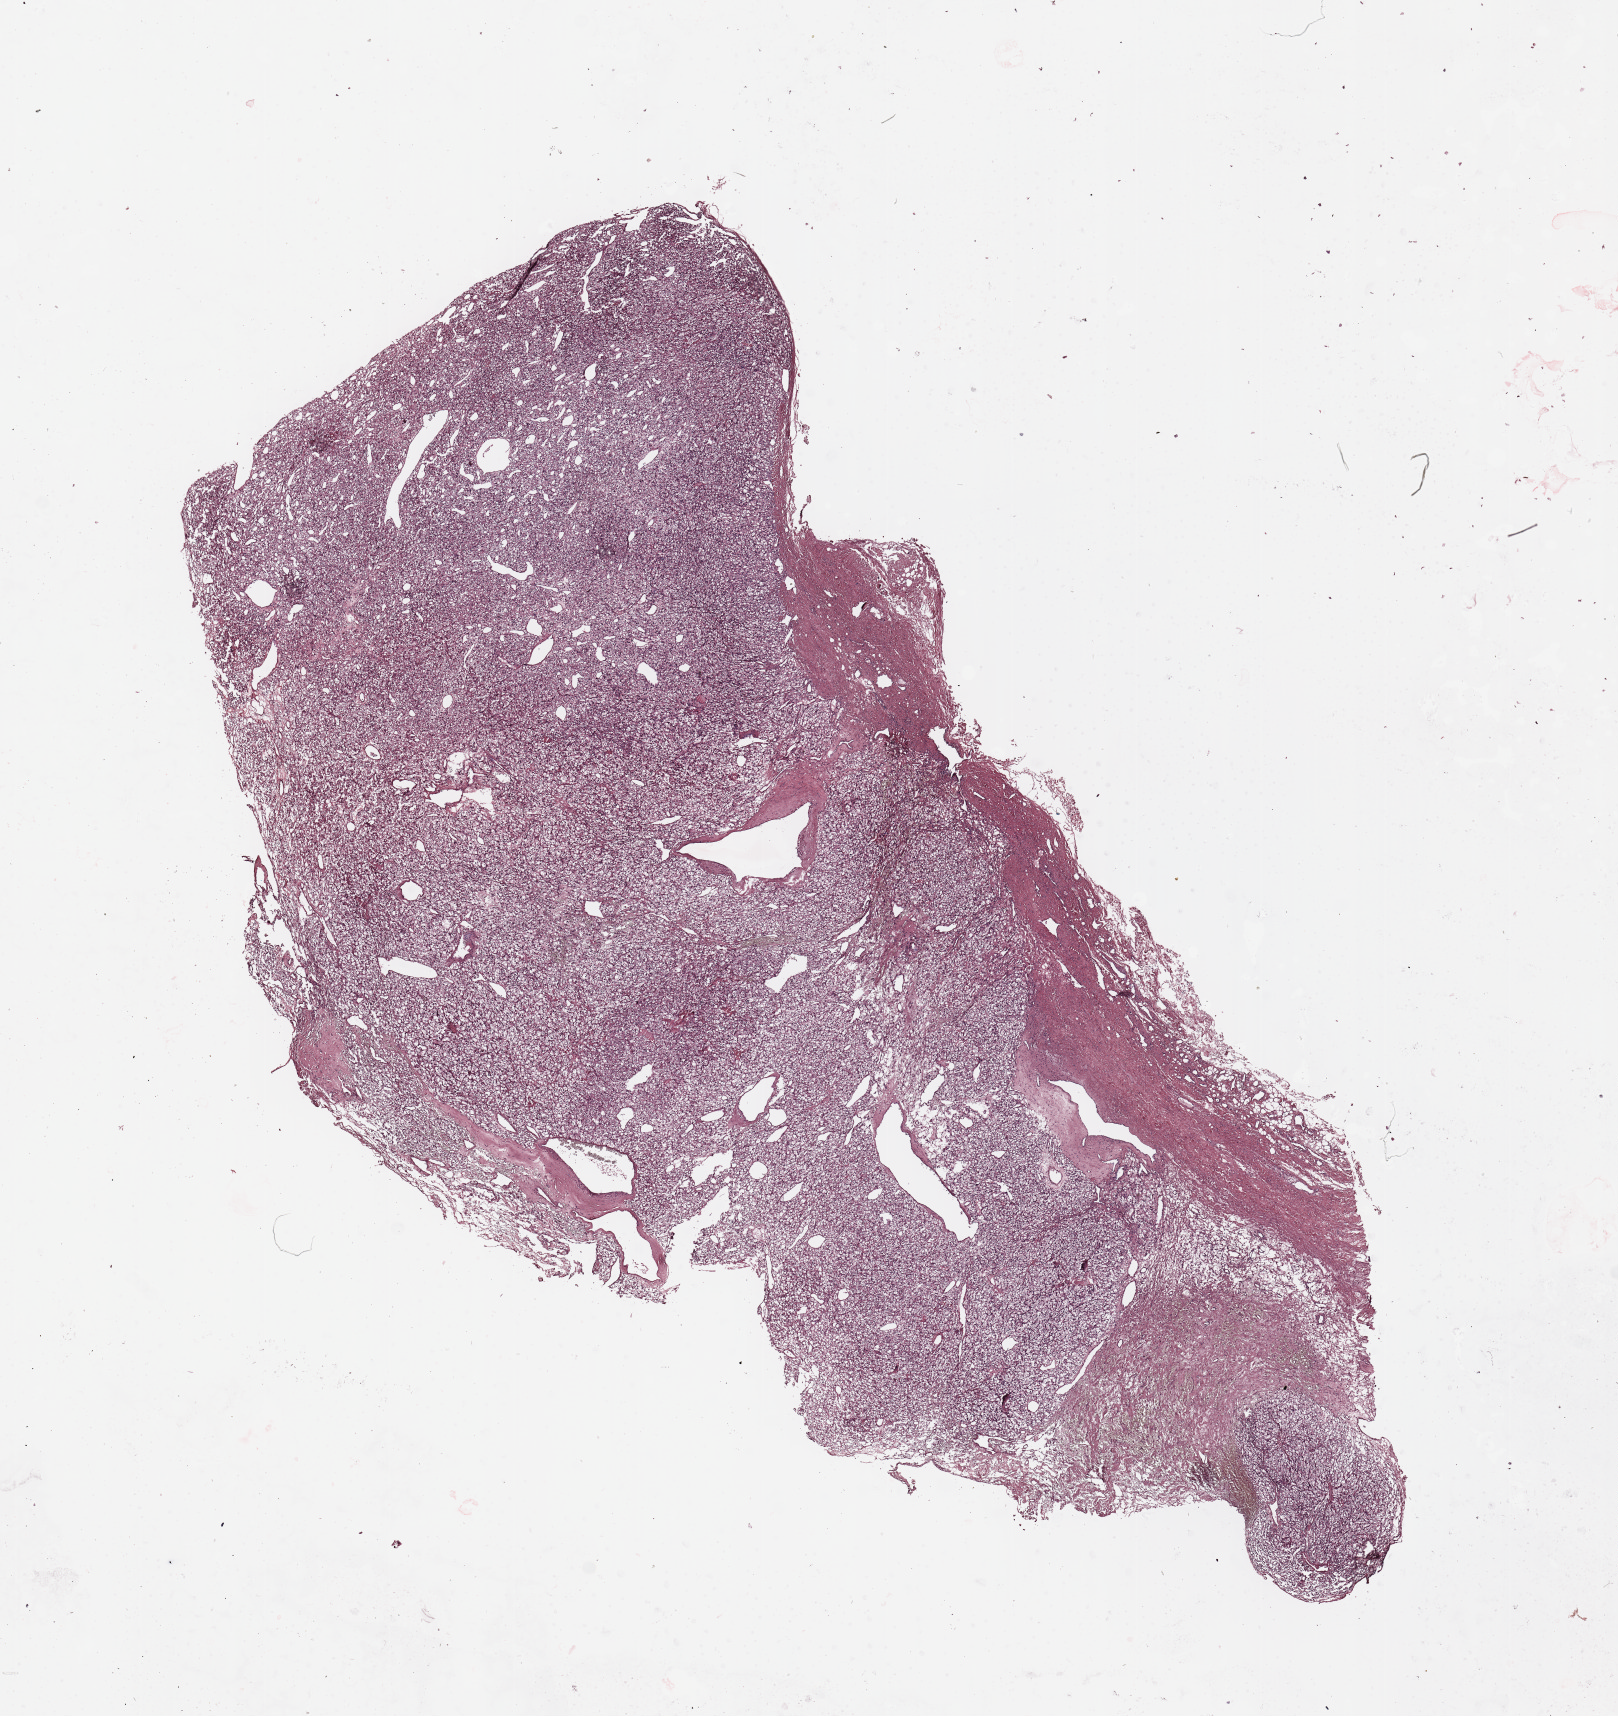
Digitized H&E-stained tissue section (whole slide) — whole scanned area (about 12.8 x 13.6 mm, acquisition: 20x scan) shown as a low-resolution overview. Tumour tissue sample, sampled site: kidney. Male, 67 y/o. Histologic grade: G1 (well differentiated). Pathologist review of this section (percent, as recorded): tumour nuclei 90%, necrosis 5%.
Primary tumour site (as recorded): upper pole. Histologic diagnosis: Renal cell carcinoma, NOS. AJCC pathologic stage: I.